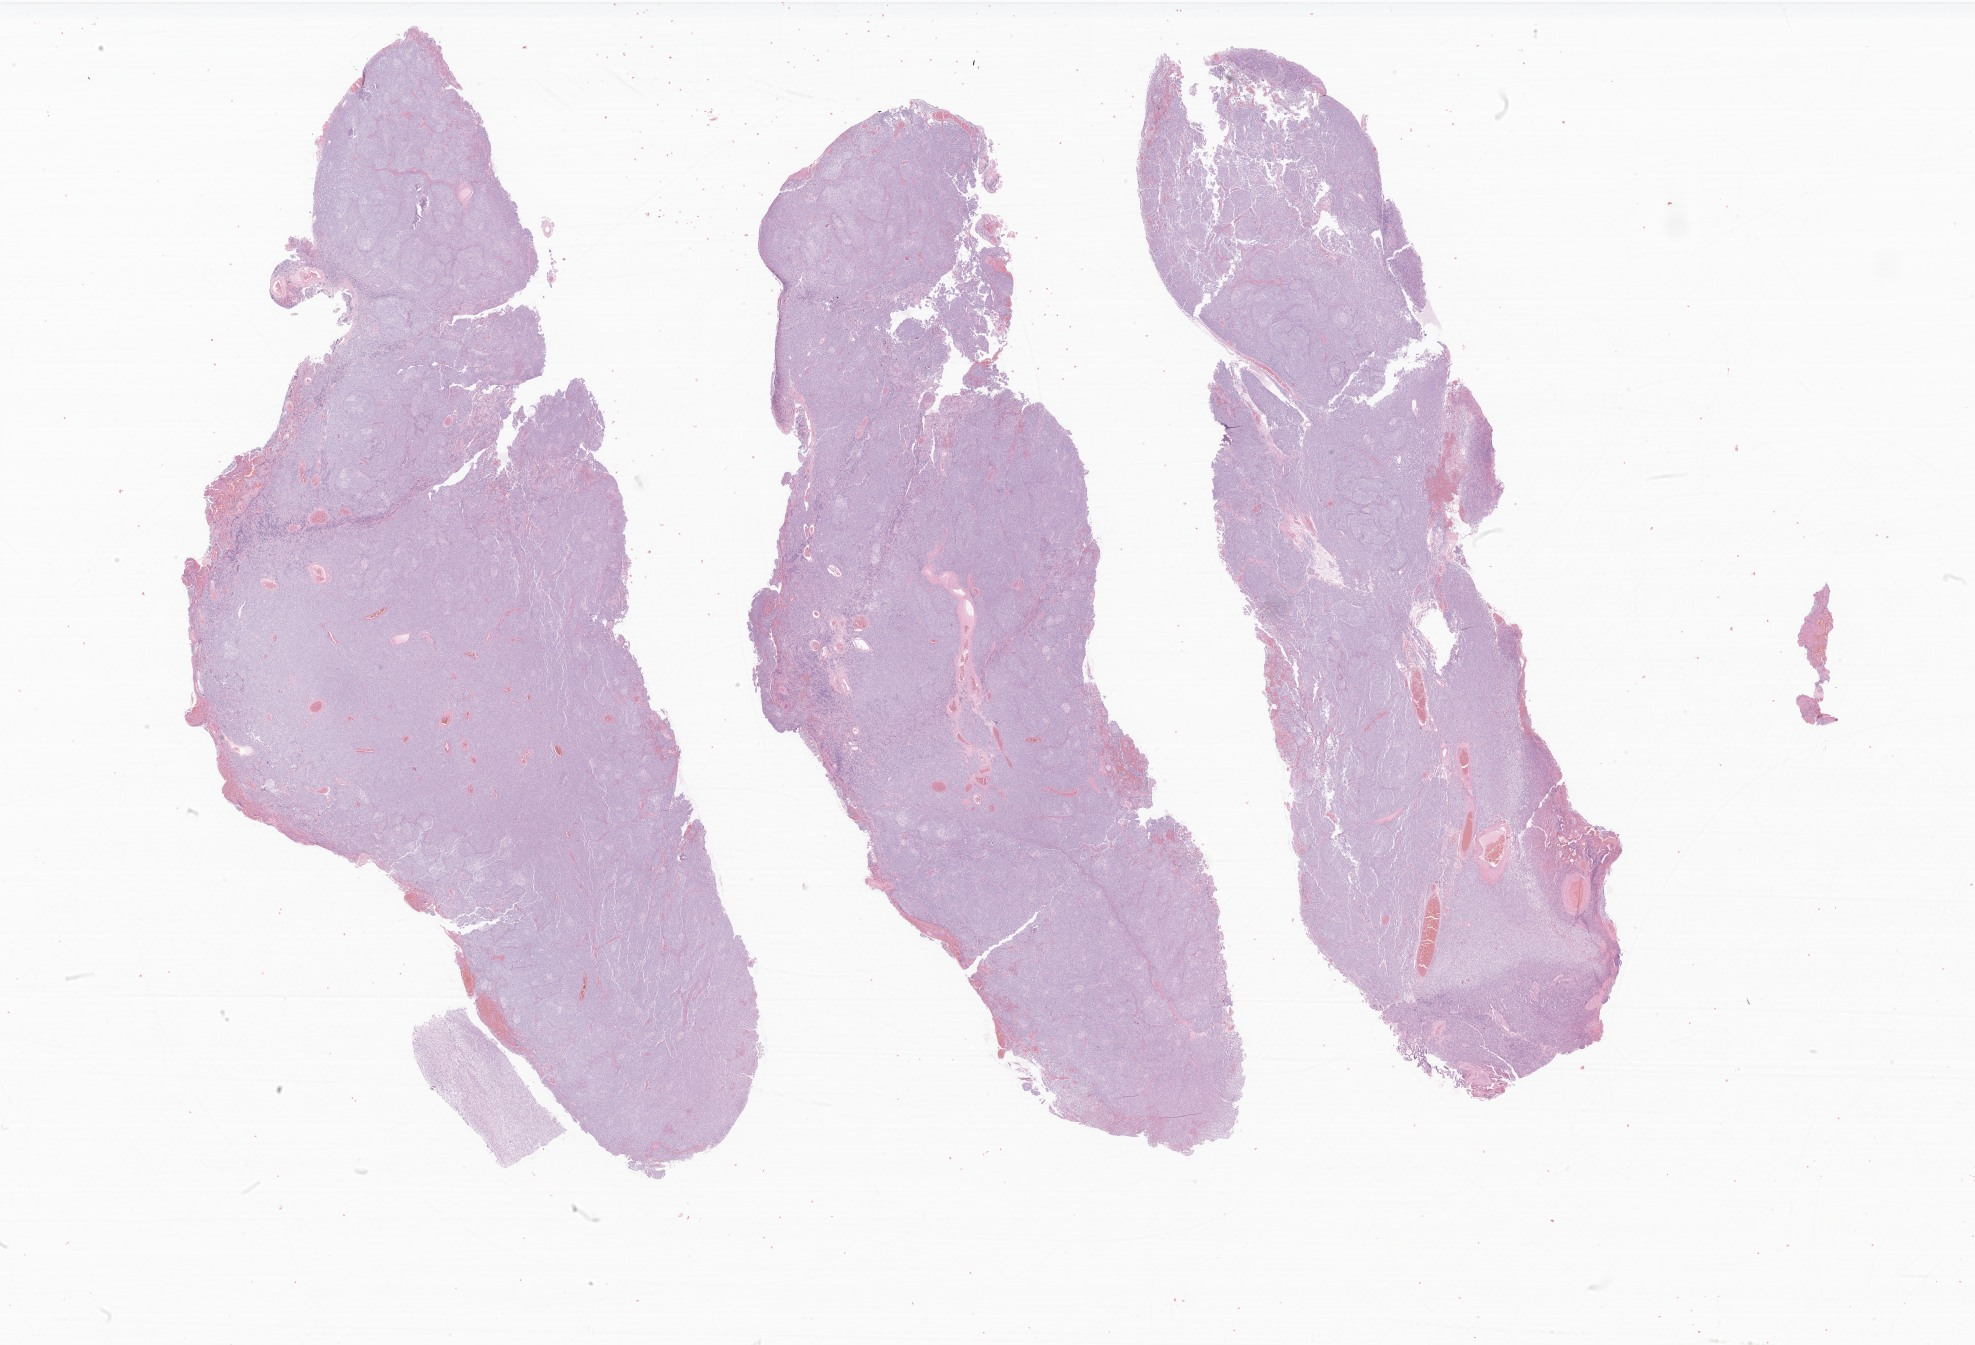
Hematoxylin and eosin (H&E) whole-slide image of tumor tissue from the brain, low-resolution overview of the scanned area, about 33.3 x 22.7 mm. Formalin-fixed, paraffin-embedded (FFPE) tissue. Male patient, age 84 months.
Diagnosis (ICD-O-3 morphology term): Medulloblastoma, NOS.